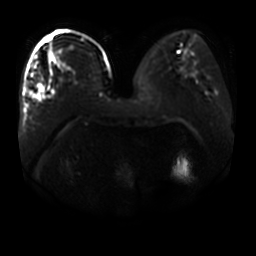
Breast MRI, one axial slice; slice 19 of 44 in the series (ordered by position); diffusion-weighted series; image 2 of 4 stored at this slice position (different b-values; order by instance number); 3 T; 5 mm slice thickness; 256 × 256 image matrix, field of view 400 × 400 mm. Female patient.
Outlined on this slice (manually delineated by an expert):
- tumour on diffusion-weighted imaging: box from (x=37, y=84) to (x=43, y=92) px